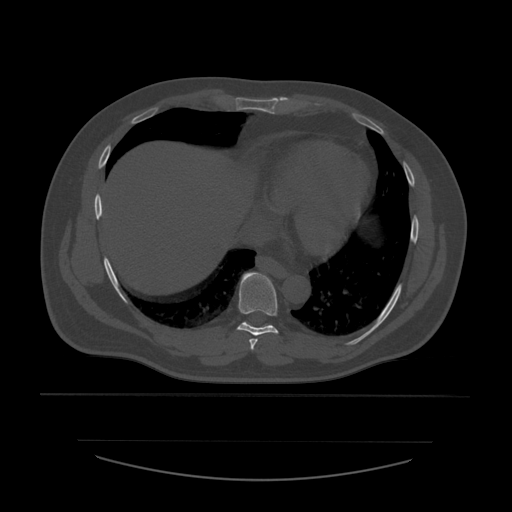
CT including the spine, one axial slice; position 336 of 532 along the scan axis; reconstruction kernel STANDARD; 120 kVp; bone window (W 1800 / L 400 HU); 512 × 512 image matrix, field of view 441 × 441 mm. Patient age 44 years. From the clinical record (not read from this slice): primary cancer: soft tissue sarcoma.
Outlined on this slice (semi-automatic segmentation, software-assisted and operator-edited):
- T7 vertebra: box from (x=249, y=339) to (x=258, y=350) px
- T8 vertebra: (x=237, y=273)–(x=279, y=336)